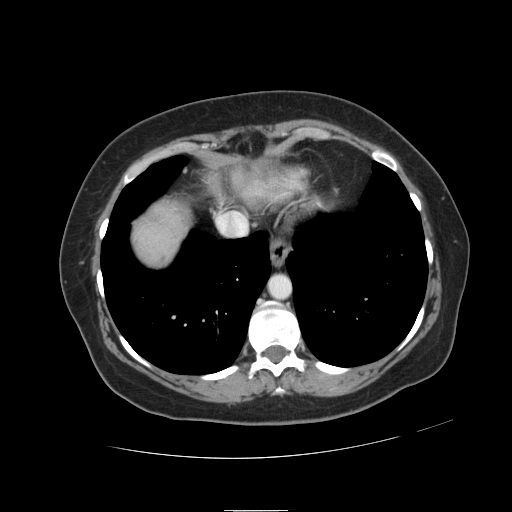
Contrast-enhanced abdominal CT, one axial slice. Slice 111 of 121 in the series (ordered by position). Soft-tissue window (W 400 / L 40 HU). 2.5 mm slice thickness. 512 × 512 image matrix. Female patient, age 52 years. Case-level facts recorded for this patient, not image findings: diagnosis: colorectal cancer liver metastases, imaged before liver resection; multiple liver metastases: yes; largest metastasis: 6.3 cm; disease in both lobes: no.
Structures marked on this image (outlined manually by an expert reader):
- liver: bounding box (x1, y1, x2, y2) in pixels: (134, 205, 186, 265)